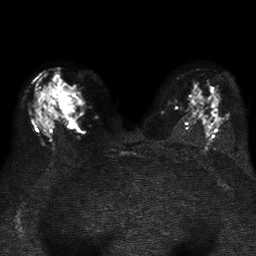
Breast MRI, one axial slice; position 21 of 37 along the scan axis; diffusion-weighted series; image 2 of 4 stored at this slice position (different b-values; order by instance number); 1.5 T; 5 mm slice thickness; 256 × 256 image matrix, field of view 320 × 320 mm. Female patient.
Structures marked on this image (manually delineated by an expert):
- tumour on diffusion-weighted imaging: bounding box (x1, y1, x2, y2) in pixels: (59, 97, 73, 113)